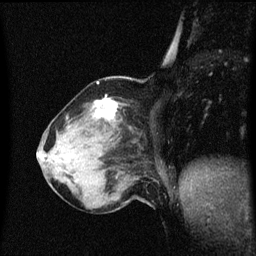
Breast MRI (dynamic contrast-enhanced), one sagittal slice; position 20 of 60 along the scan axis; dynamic contrast-enhanced series, image 2 of 3 at this slice position (ordered by acquisition); 1.5 T; TE 4.2 ms, TR 8.4 ms; 2 mm slice thickness; 256 × 256 image matrix, field of view 200 × 200 mm. Female patient, age 64 years. Case-level facts recorded for this patient, not image findings: setting: breast cancer imaged before/during neoadjuvant chemotherapy; receptor status: HR-positive, HER2-negative.
Outlined on this slice (semi-automatically segmented with operator editing):
- analysis volume of interest (the breast-tissue region the enhancement analysis was run in; not a lesion): bounding box <58,98,133,167> (left, top, right, bottom; pixels)
- tumour enhancement mask (voxels above the 70 % enhancement threshold inside the analysis volume of interest): <96,98,117,121>